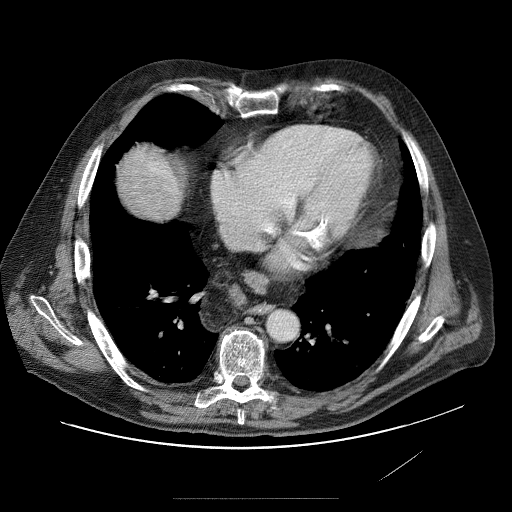
Contrast-enhanced abdominal CT (liver protocol), one axial slice; position 81 of 89 along the scan axis; 120 kVp; soft-tissue window (W 400 / L 40 HU); 512 × 512 image matrix. Case-level facts recorded for this patient, not image findings: diagnosis: hepatocellular carcinoma (patient treated with transarterial chemoembolisation; whether this scan precedes or follows treatment is not stated here); TNM stage (as recorded): Stage-IVA; Child-Pugh class: A; tumour differentiation: moderately differentiated; tumour nodularity: multinodular.
Annotated regions visible in this slice (semi-automatic segmentation, software-assisted and operator-edited):
- liver parenchyma outside the tumour (the mass and vessels are separate outlines, so this box may not span the whole liver): bounding box [x1, y1, x2, y2] px = [130, 154, 174, 200]